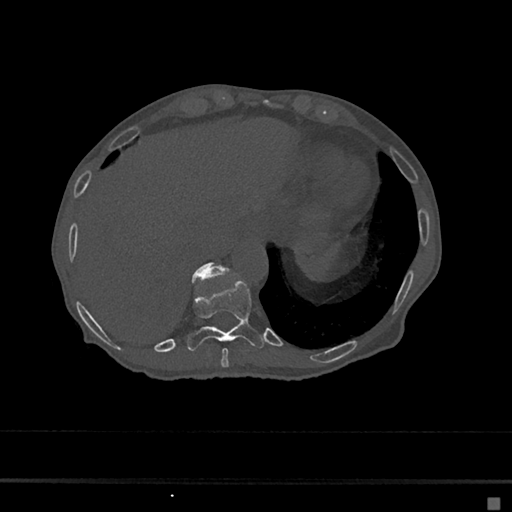
CT including the spine, one axial slice. Slice 225 of 797 in the series (ordered by position). Reconstruction kernel Br40s/3. Bone window (W 1800 / L 400 HU). 0.5 mm slice thickness. 512 × 512 image matrix. Patient: female, 68 years. From the clinical record (not read from this slice): primary cancer: renal.
Structures marked on this image (semi-automatic segmentation, software-assisted and operator-edited):
- T10 vertebra: bounding box [x1, y1, x2, y2] px = [187, 280, 264, 351]
- T11 vertebra: [192, 262, 227, 283]
- T9 vertebra: [221, 348, 229, 367]